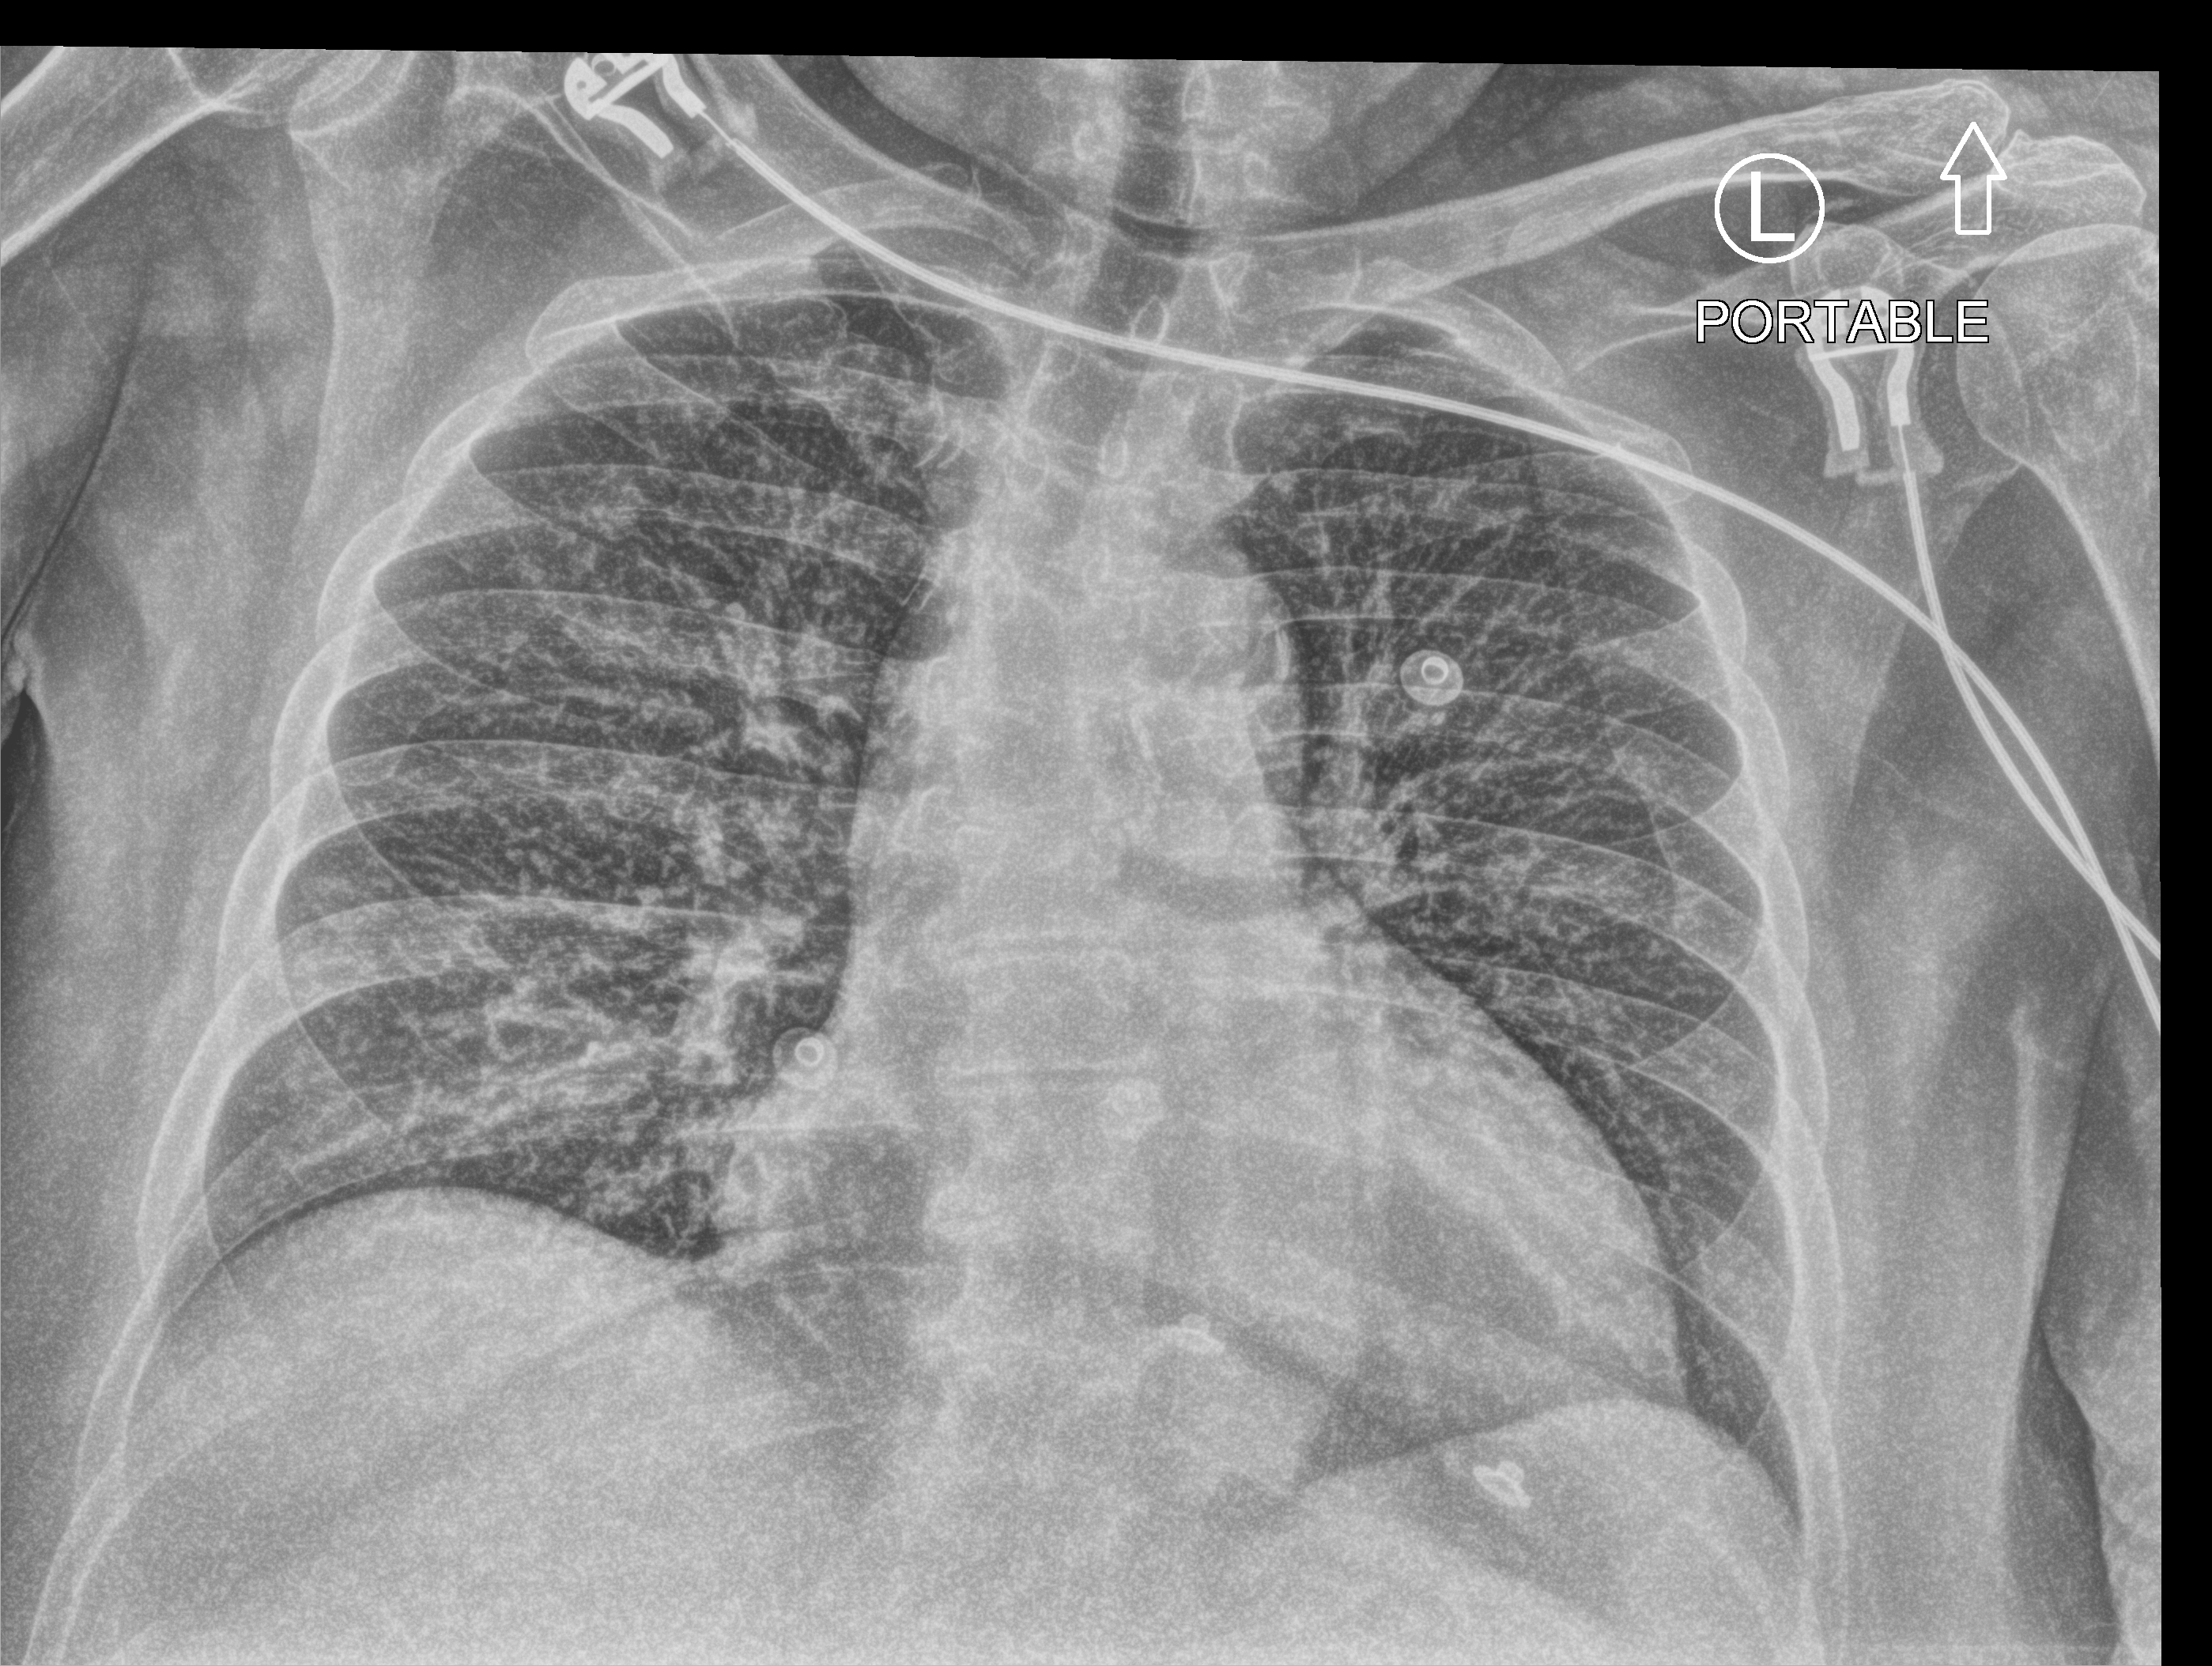
Bedside chest radiograph (computed radiography), anteroposterior (AP) projection. Female patient hospitalised with COVID-19, age 60–74 years.
From the hospital-stay record, not from the radiograph (when in the stay this image was taken is not recorded):
- mechanically ventilated during this hospital stay: no
- chronic kidney disease (admission record): no
- admitted to intensive care during this hospital stay: no